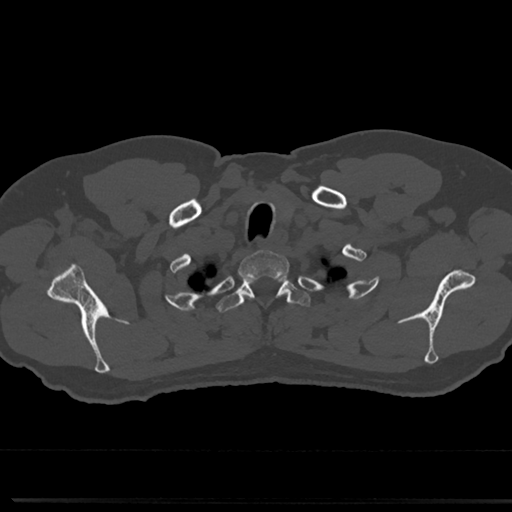
CT including the spine, one axial slice. Reconstruction kernel Br40s/3. 120 kVp. Bone window (W 1800 / L 400 HU). 512 × 512 image matrix. Patient: male, 61 years. Case-level facts recorded for this patient, not image findings: primary cancer: prostate.
Structures marked on this image (semi-automatically segmented with operator editing):
- T1 vertebra: bounding box [x1, y1, x2, y2] px = [242, 251, 287, 269]
- T2 vertebra: [223, 274, 305, 323]